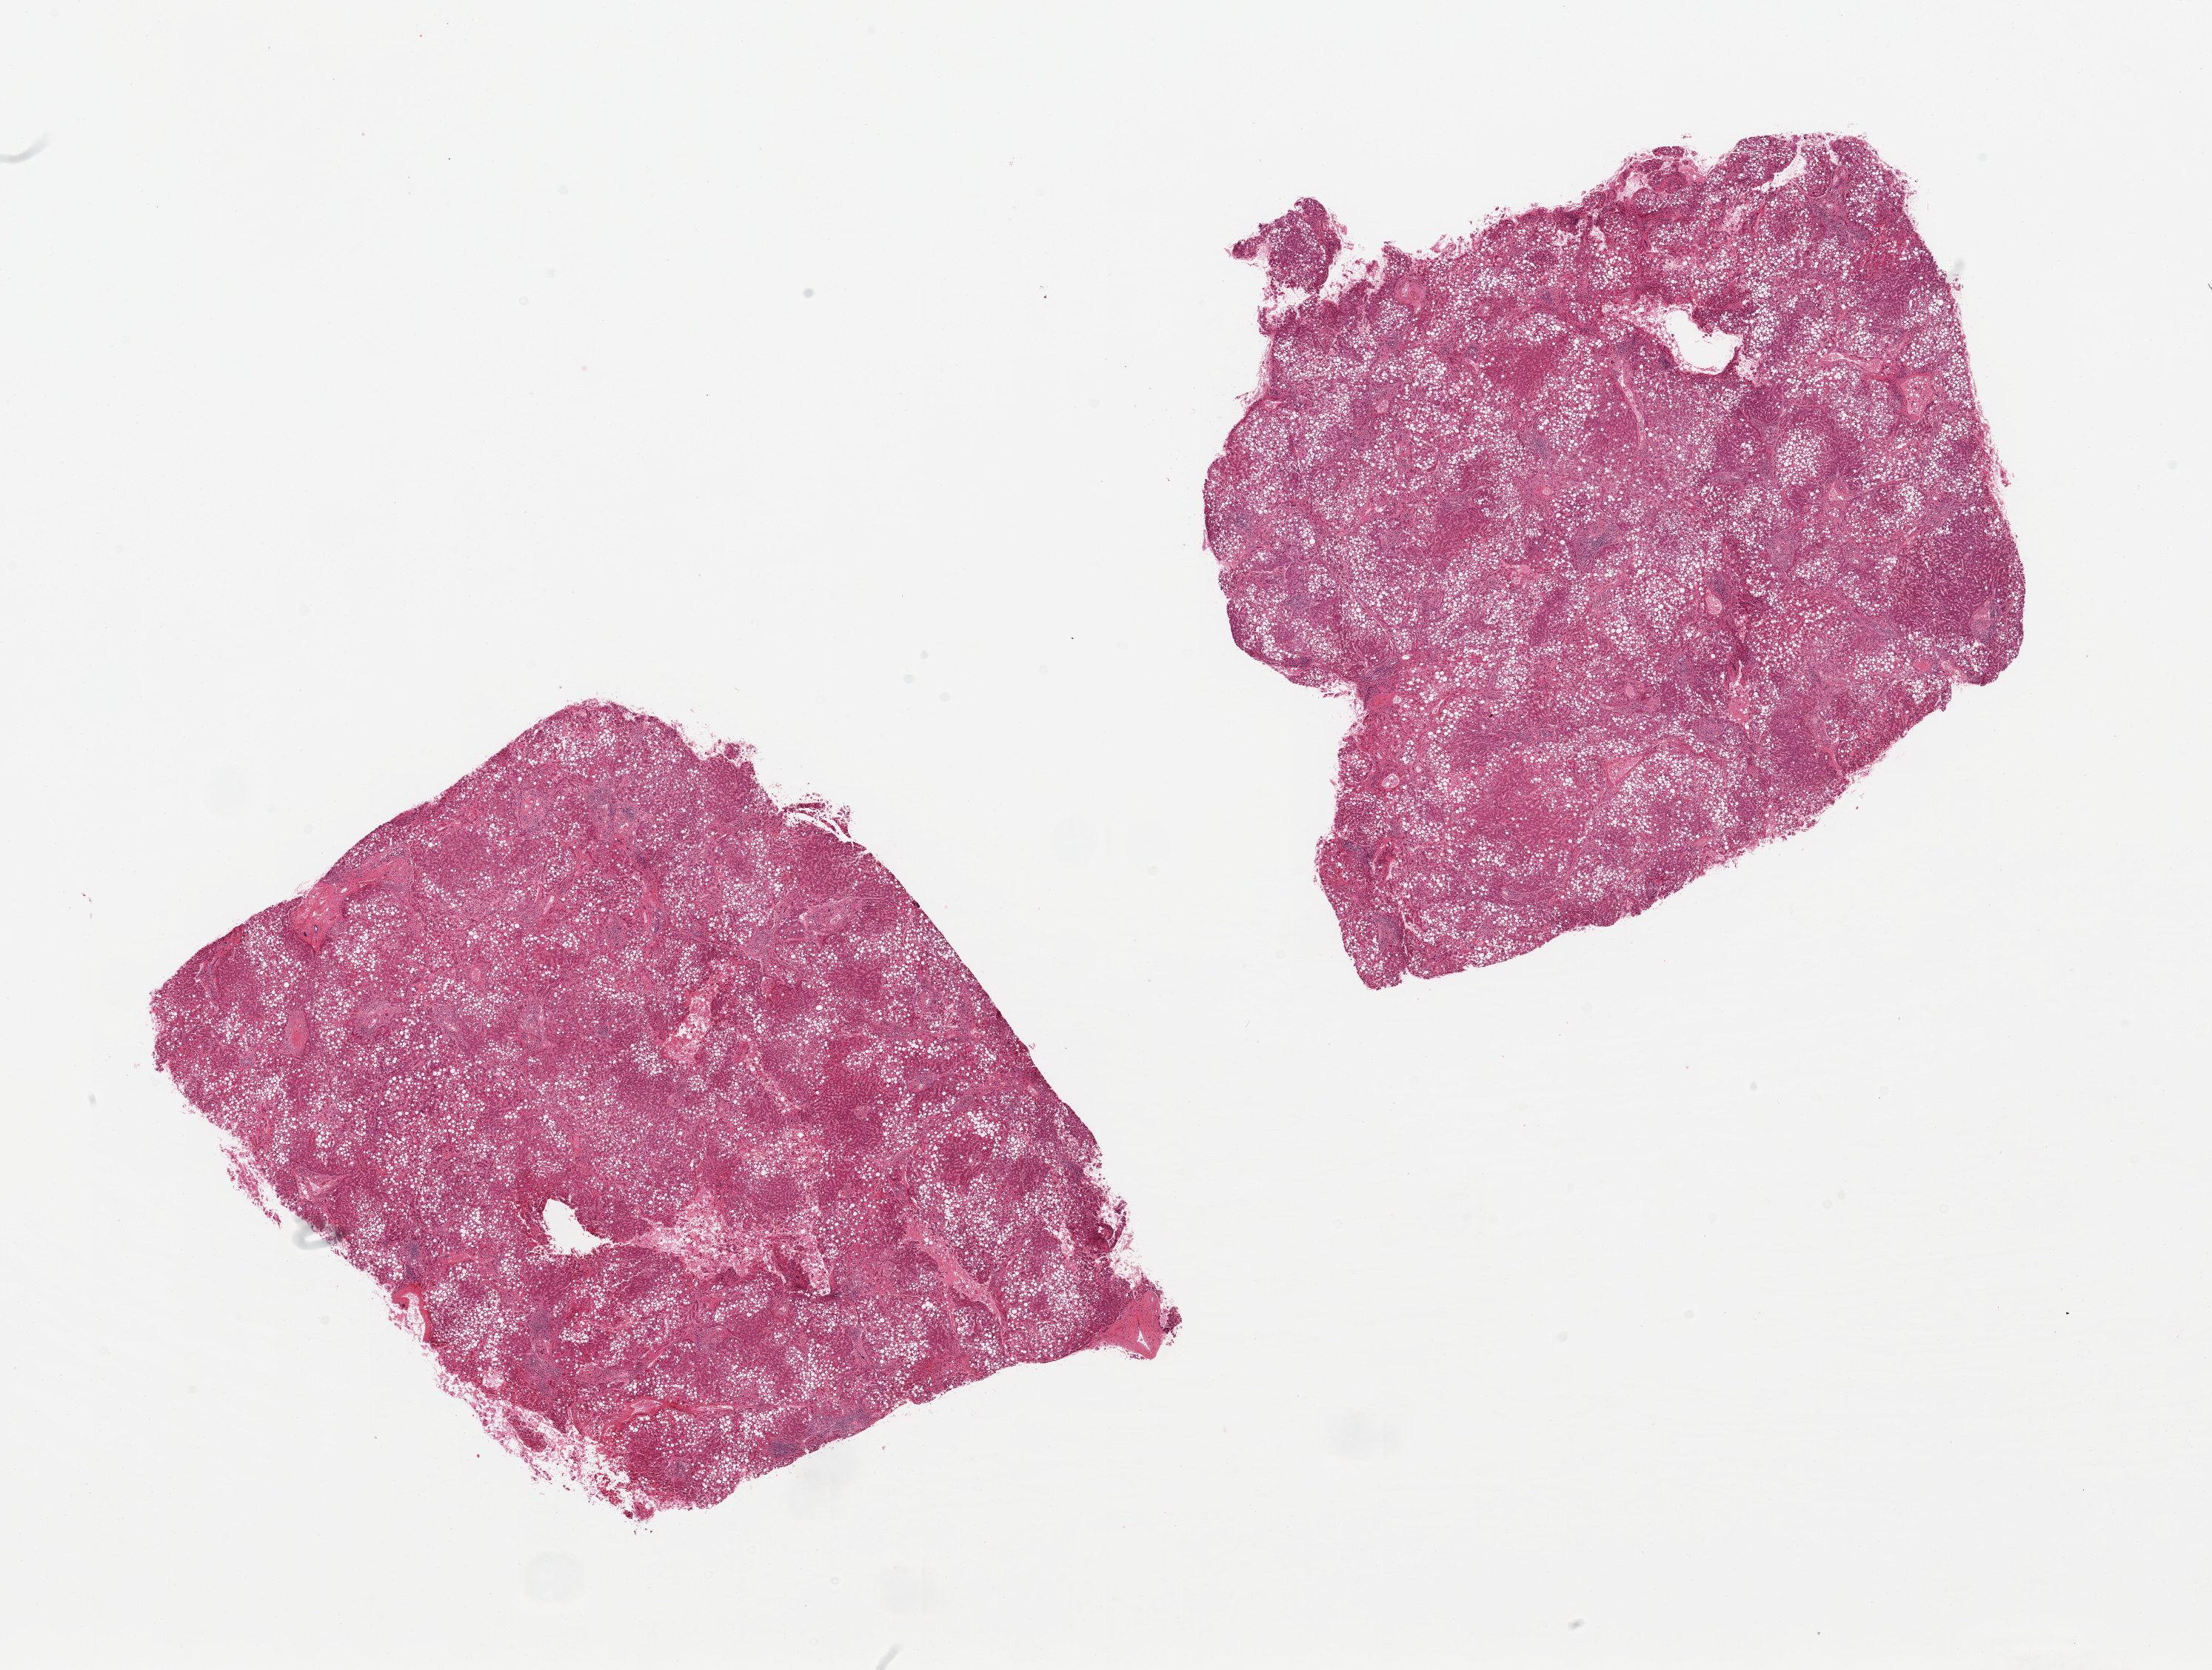
Digitized haematoxylin and eosin-stained section — low-resolution overview of the scanned area, about 23.6 x 17.8 mm. PAXgene-fixed, paraffin-embedded tissue. Section of liver (target tissue). Tissue donor sample. Male donor.
Pathologist's review note for this sample: 2 pieces; steatosis, bridging fibrosis, and chronic inflammation (?Nonalcoholic steatohepatitis).